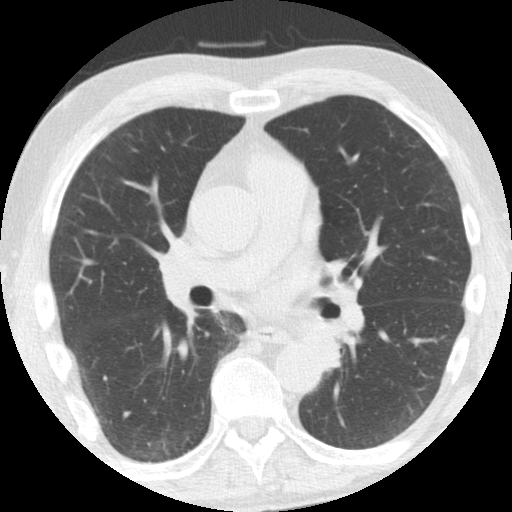
Low-dose screening chest CT, axial slice, third annual screen, lung window (W 1500 / L -600 HU), 2.5 mm slice thickness. Male, age 61 years at enrolment. Former smoker at enrolment.
Lesion marked by an expert reader, box from (x=295, y=316) to (x=345, y=362) px. No non-calcified nodule or mass ≥4 mm was recorded by the screening reader at this exam. Later outcome: lung cancer diagnosed 363 days after this screen — squamous cell carcinoma, NOS, left upper lobe, left lower lobe, well differentiated (G1), stage IIB (AJCC 6th edition), 100 mm at pathology.